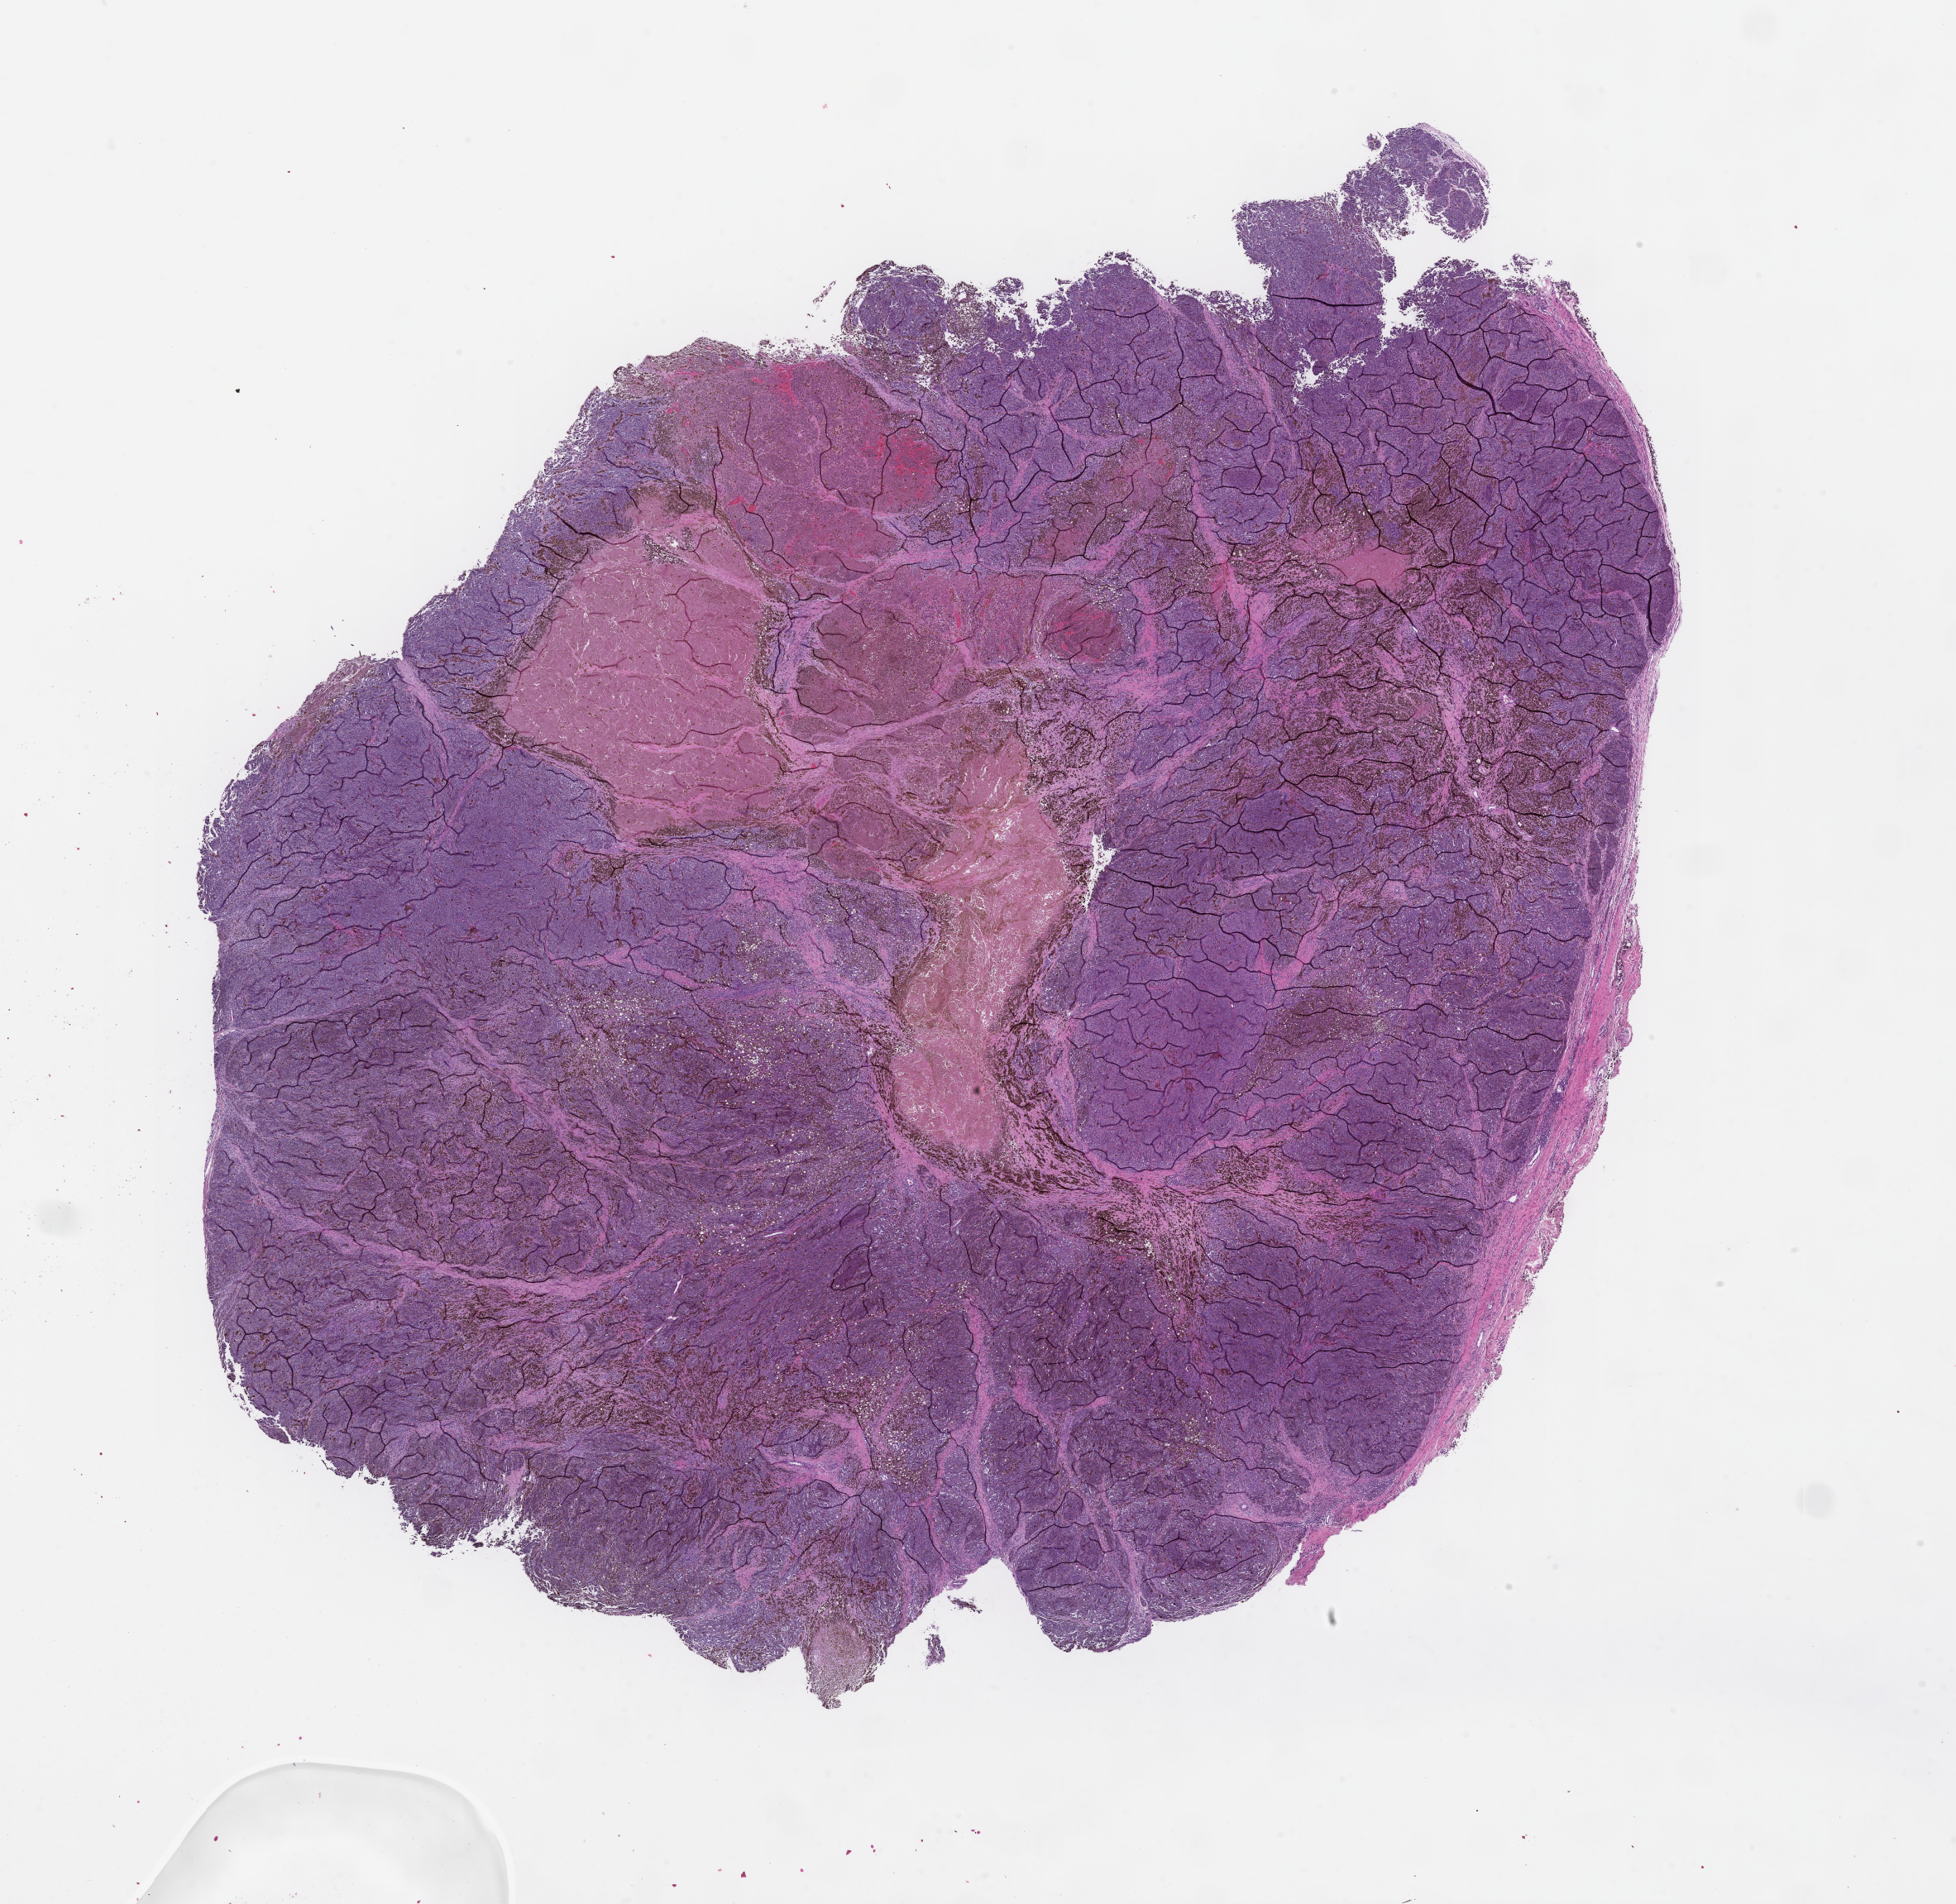
H&E whole-slide image, shown as a low-resolution overview of the whole scanned area (about 19.1 x 18.6 mm), formalin-fixed, paraffin-embedded (FFPE) tissue, tissue site: skin. Patient: male.
• patient diagnosis: Melanoma